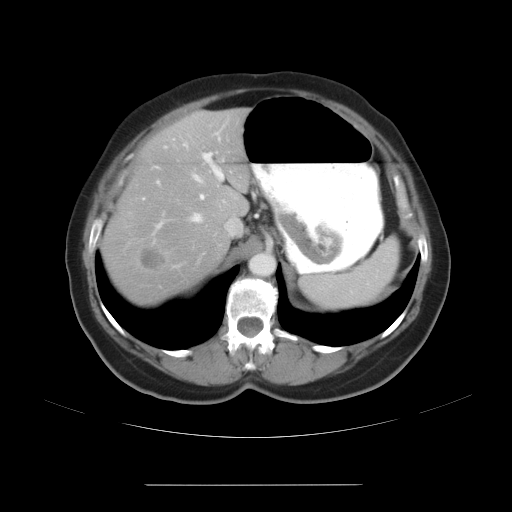
Contrast-enhanced abdominal CT, one axial slice. Position 20 of 27 along the scan axis. Reconstruction kernel STANDARD. Soft-tissue window (W 400 / L 40 HU). 512 × 512 image matrix. Female patient, age 58 years. Case-level facts recorded for this patient, not image findings: diagnosis: colorectal cancer liver metastases, imaged before liver resection; multiple liver metastases: yes; largest metastasis: 1.9 cm; chemotherapy before resection: yes.
Structures marked on this image (expert manual segmentation):
- hepatic veins: box from (x=128, y=174) to (x=235, y=244) px
- liver: (x=104, y=111)–(x=248, y=298)
- planned liver remnant (the part of the liver to remain after resection): (x=122, y=116)–(x=248, y=224)
- portal vein (with intrahepatic branches): (x=157, y=122)–(x=227, y=227)
- liver metastasis: (x=140, y=249)–(x=166, y=272)